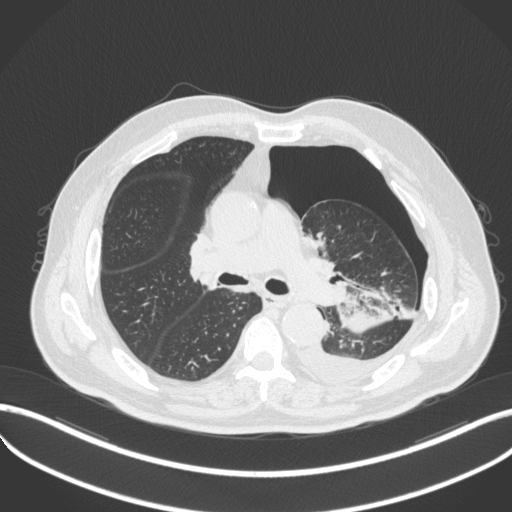
Chest CT, one axial slice. Position 313 of 466 along the scan axis. Reconstruction kernel B31f. Lung window (W 1500 / L -600 HU). 512 × 512 image matrix, field of view 400 × 400 mm. Patient: male, 76 years. From the clinical record (not read from this slice): clinical TNM (as recorded): T3 N0 M1b.
Structures marked on this image (rectangle marked by the reading radiologist):
- lung tumour (recorded histology: adenocarcinoma): box from (x=330, y=281) to (x=402, y=334) px